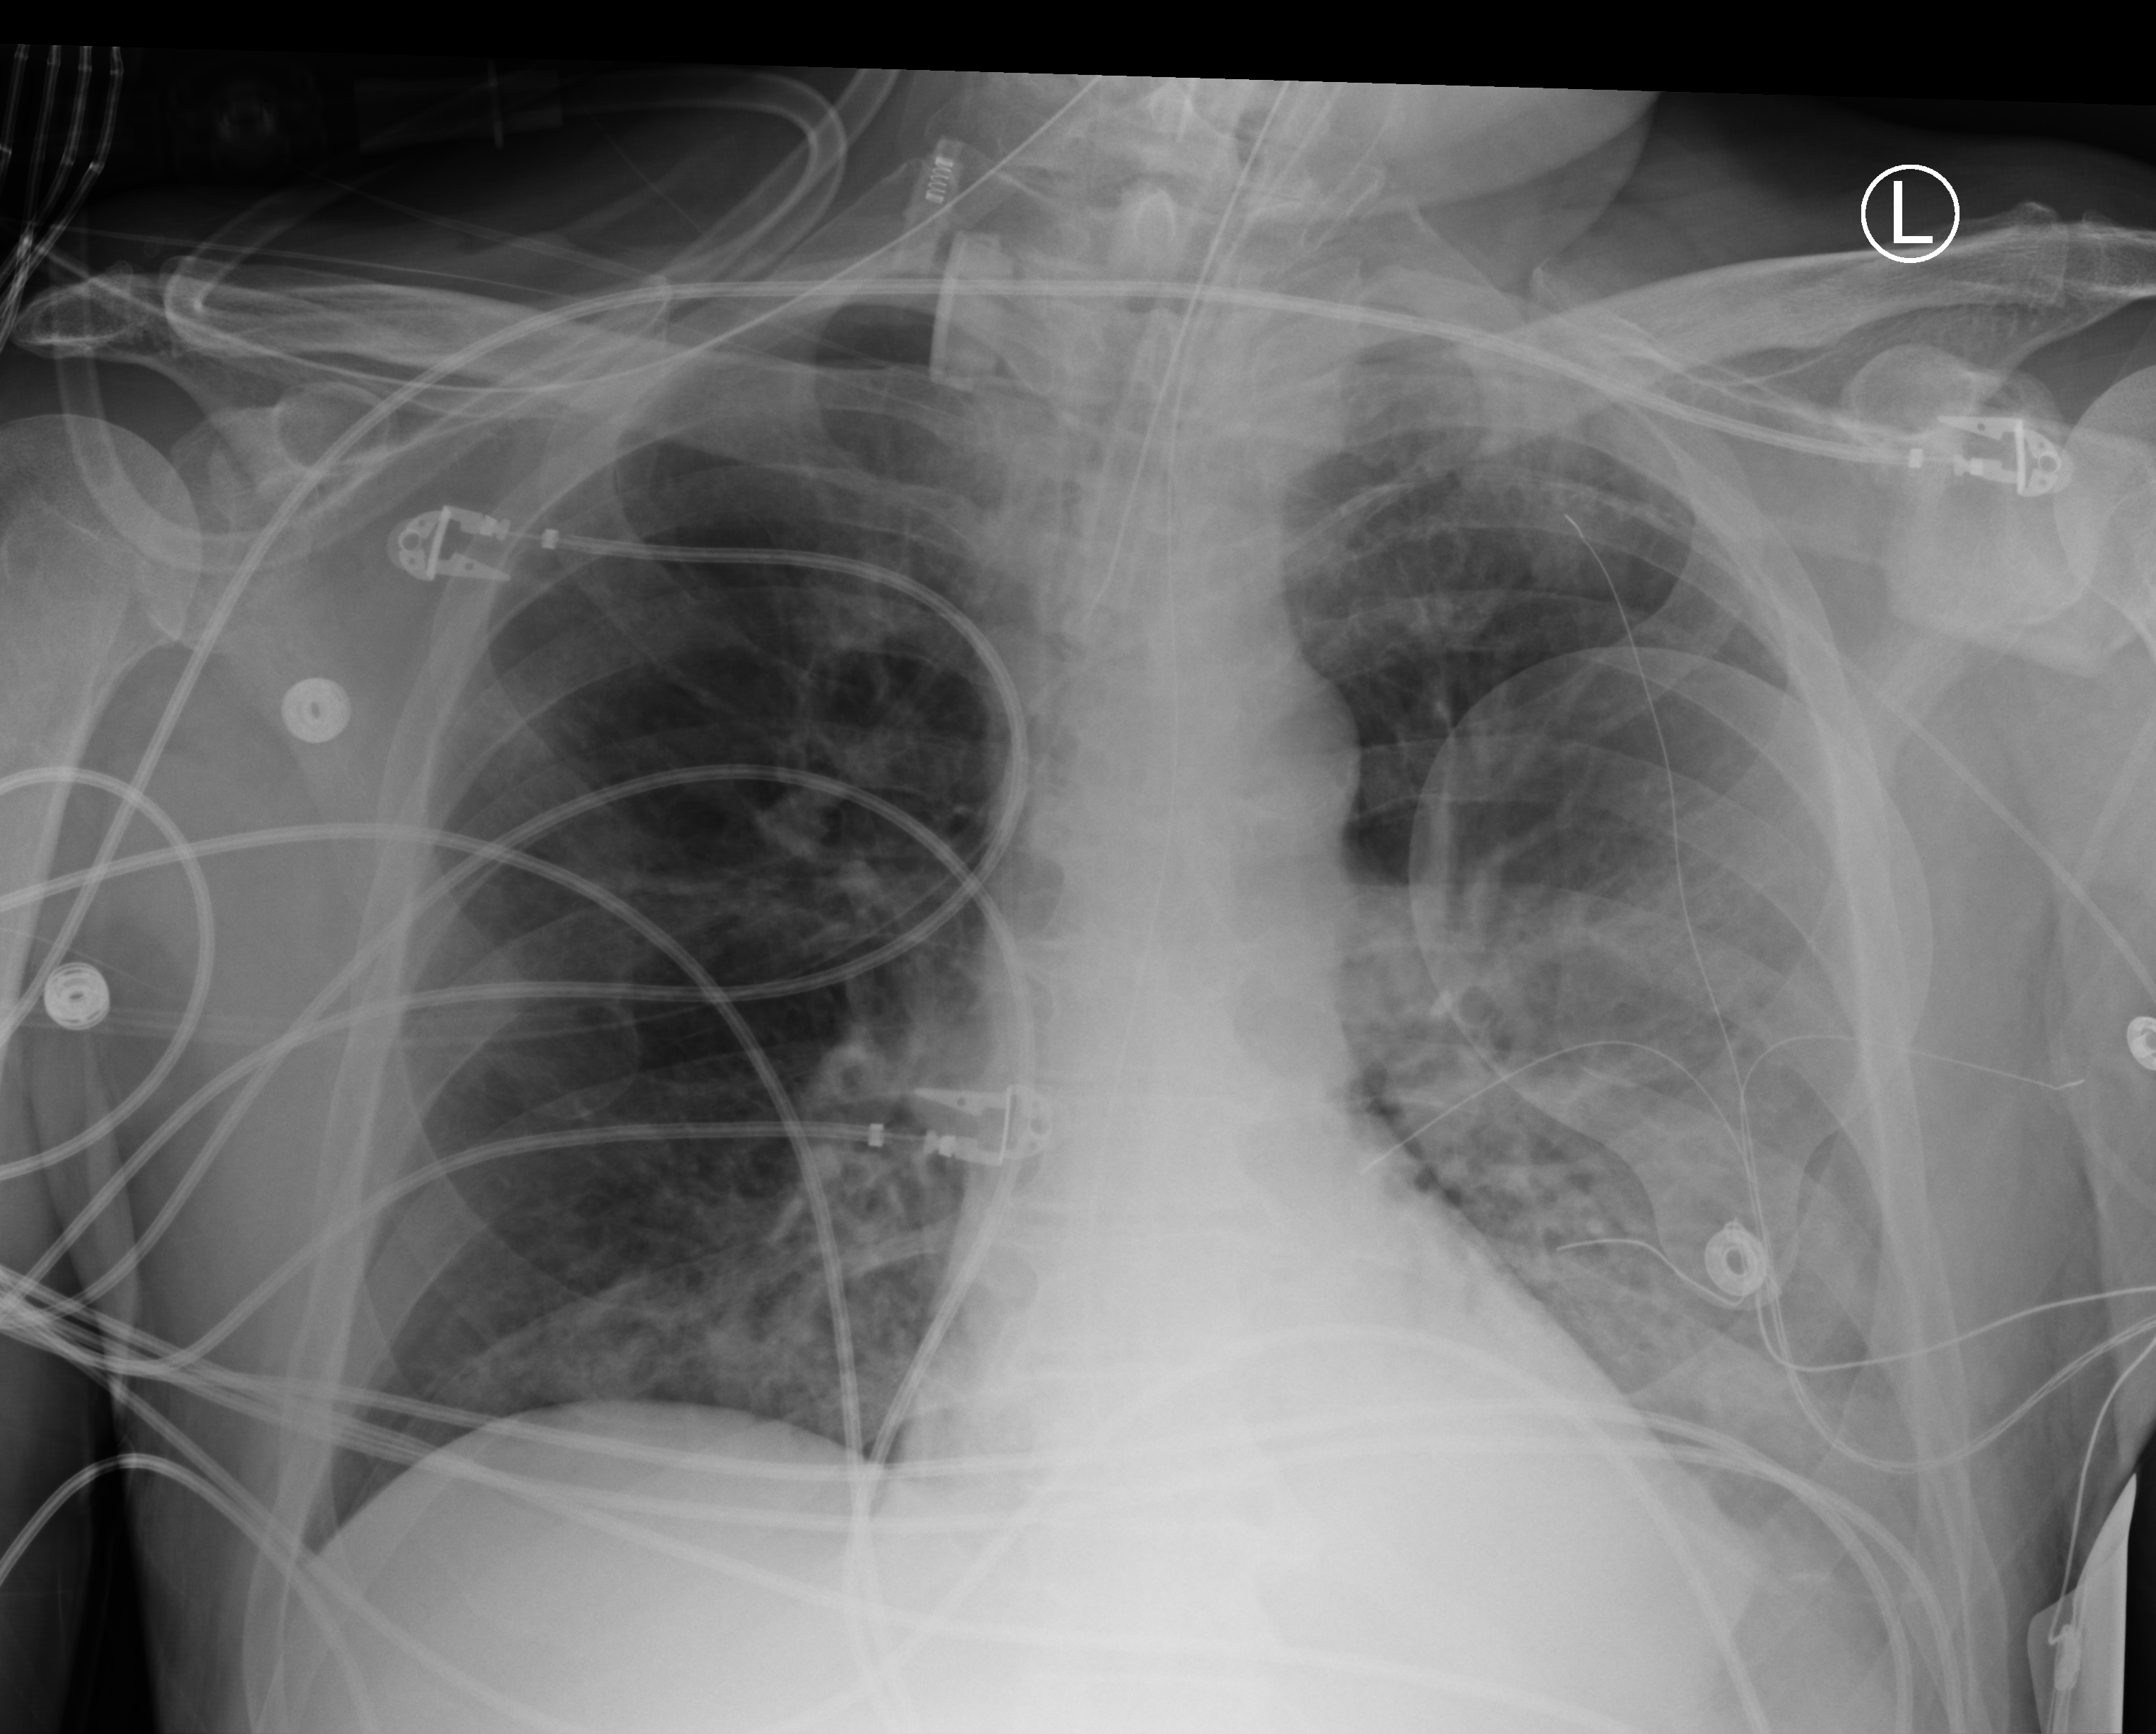
Chest X-ray (portable); anteroposterior (AP) projection. Male patient hospitalised with COVID-19, age 60–74 years.
Hospital-stay facts (about this admission, not read from this image; timing relative to this image not recorded):
- admitted to intensive care during this hospital stay: yes
- mechanically ventilated during this hospital stay: yes
- smoking status (admission record): never